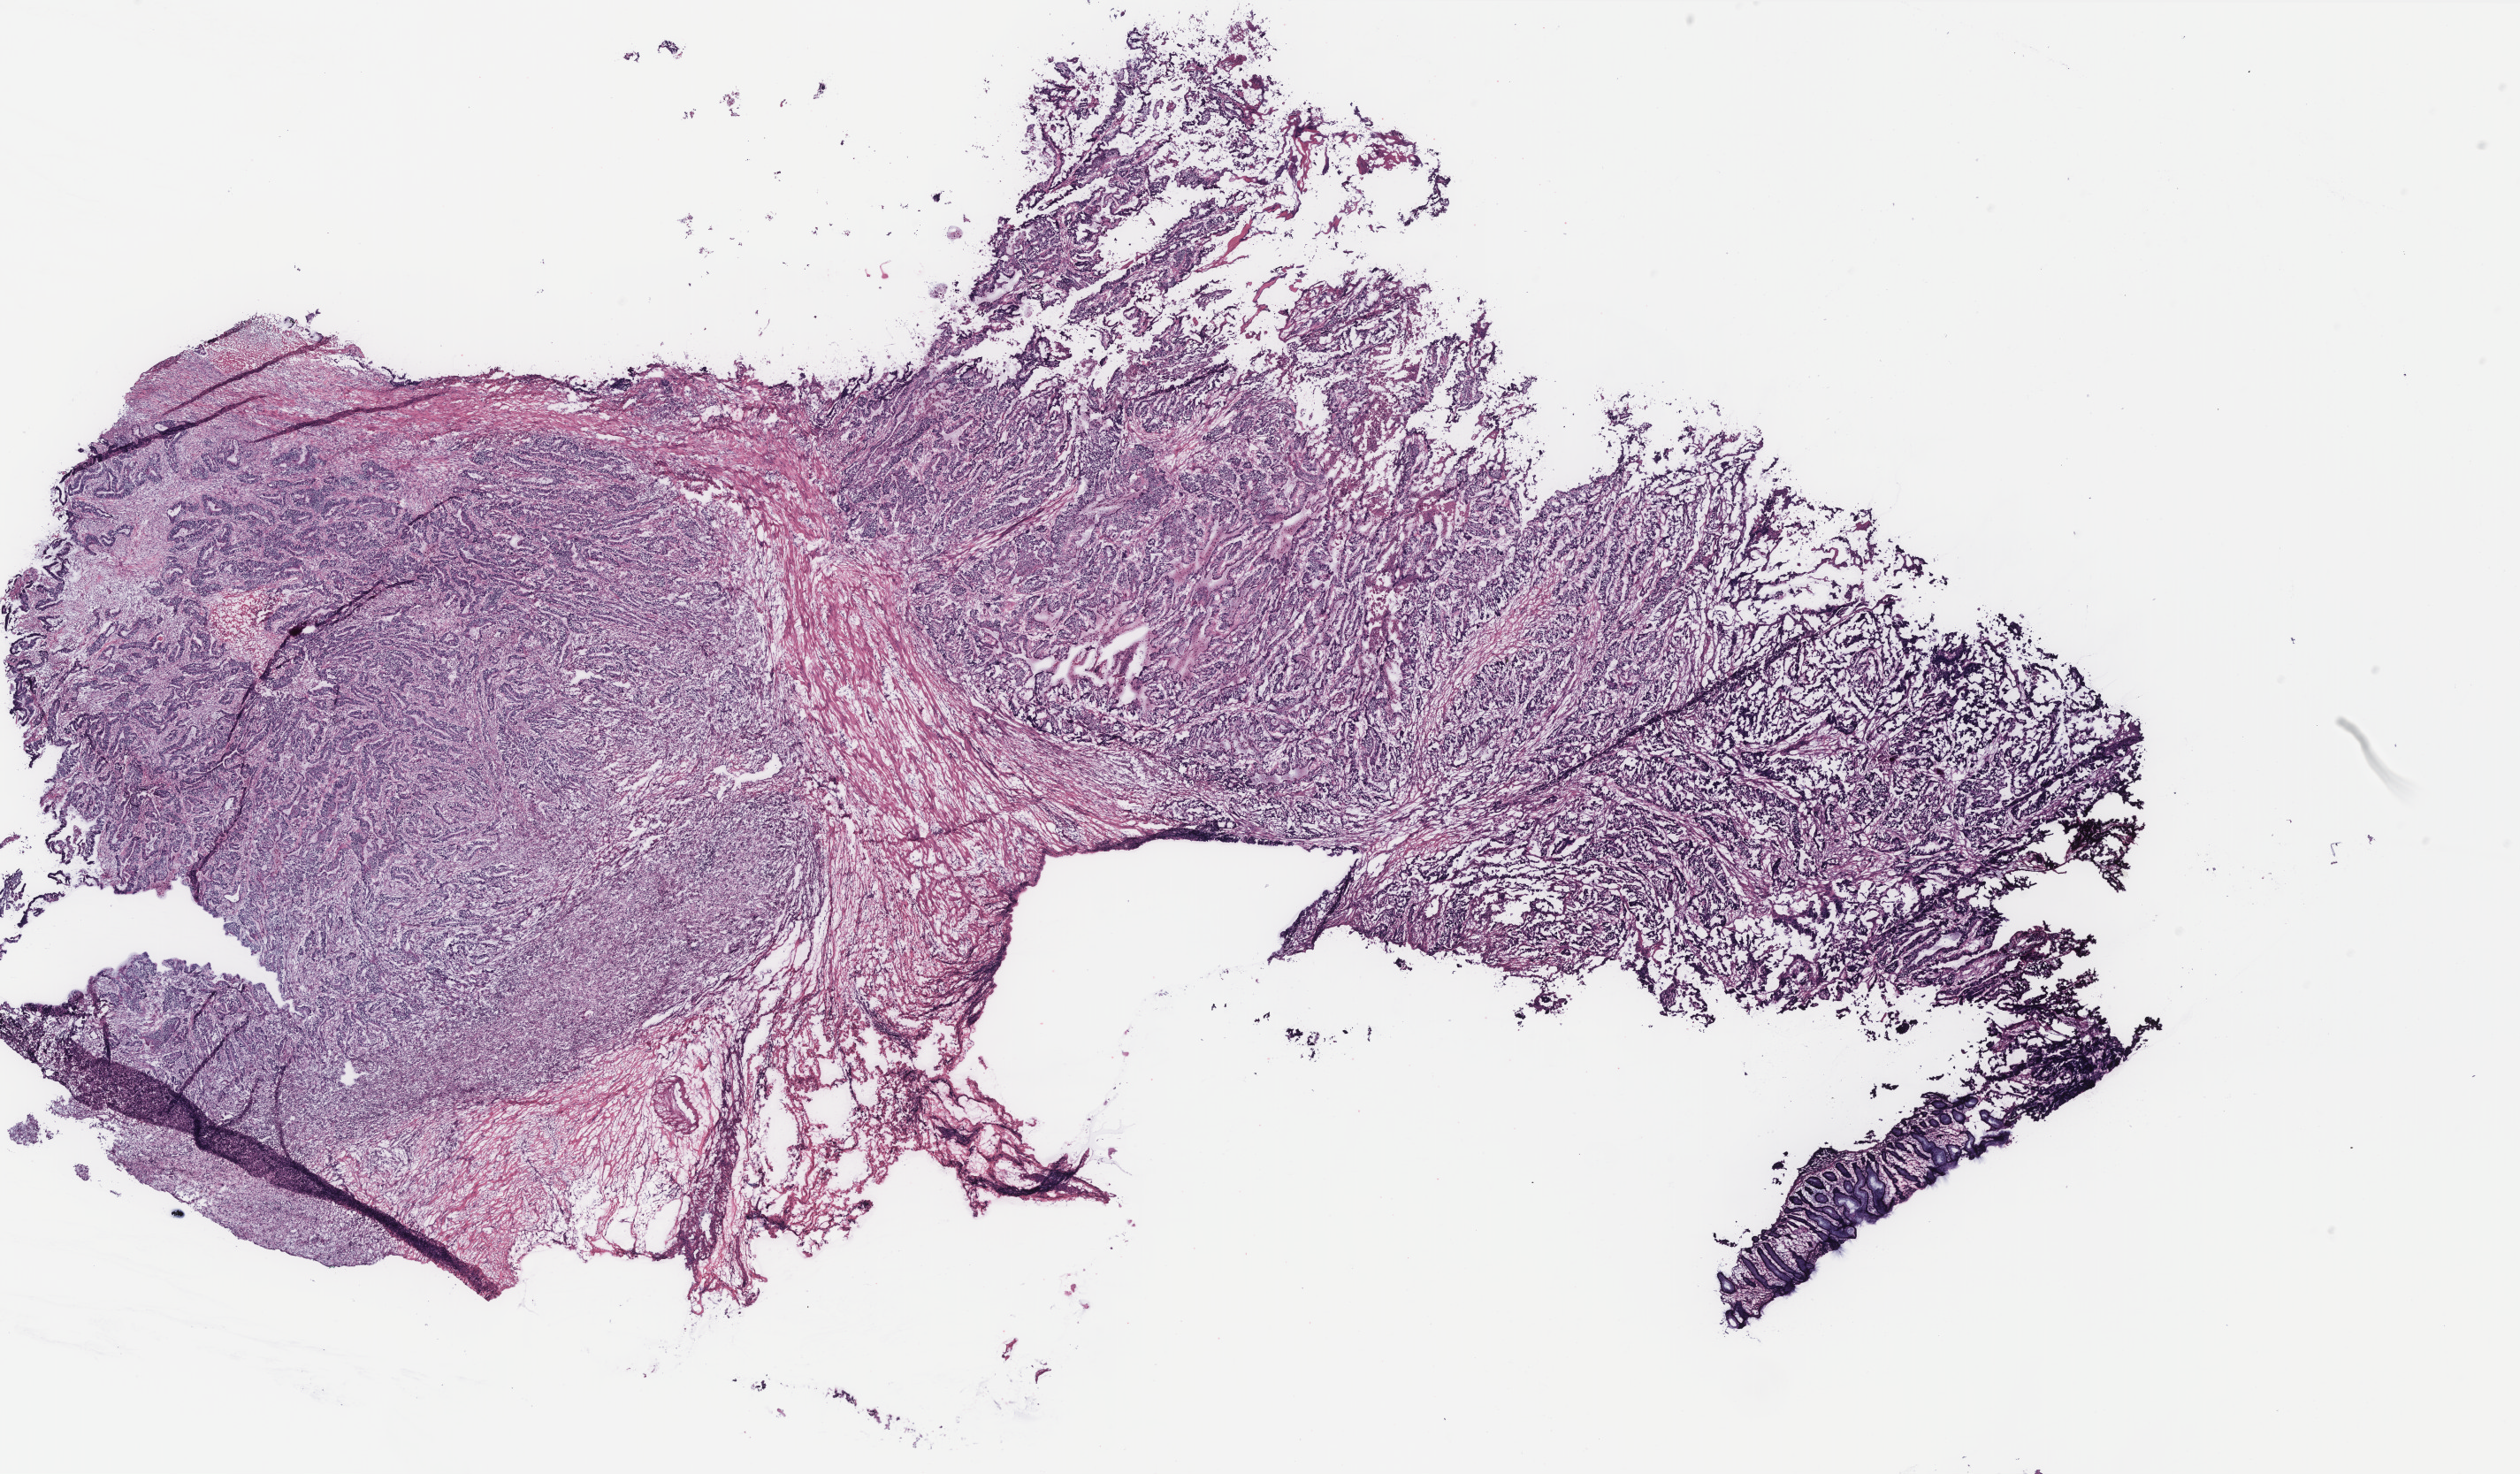
H&E-stained whole-slide image — whole scanned area (about 22.8 x 13.3 mm) shown as a low-resolution overview, colon, tissue type not recorded.
Patient diagnosis (cohort enrolment): colon cancer (colon).